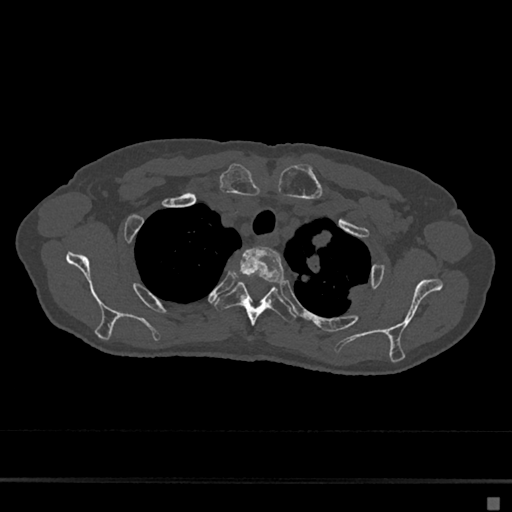
CT including the spine, one axial slice. Position 554 of 797 along the scan axis. 120 kVp. Bone window (W 1800 / L 400 HU). 0.5 mm slice thickness. 512 × 512 image matrix, field of view 360 × 360 mm. Female patient, age 68 years. From the clinical record (not read from this slice): primary cancer: renal.
Annotated regions visible in this slice (semi-automatic segmentation, software-assisted and operator-edited):
- T2 vertebra: box from (x=234, y=246) to (x=285, y=283) px
- T3 vertebra: (x=214, y=281)–(x=296, y=326)